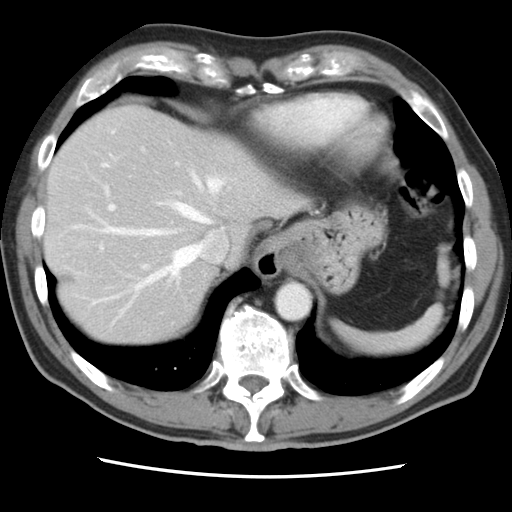
Contrast-enhanced abdominal CT, one axial slice. Position 69 of 83 along the scan axis. 120 kVp. Intravenous contrast given. Soft-tissue window (W 400 / L 40 HU). 5 mm slice thickness. 512 × 512 image matrix, field of view 321 × 321 mm. Male patient, age 69 years. Case-level facts recorded for this patient, not image findings: diagnosis: colorectal cancer liver metastases, imaged before liver resection; multiple liver metastases: yes; largest metastasis: 3.5 cm; disease in both lobes: no.
Outlined on this slice (expert manual segmentation):
- hepatic veins: bounding box (x1, y1, x2, y2) in pixels: (76, 131, 224, 311)
- liver: (45, 107, 295, 346)
- planned liver remnant (the part of the liver to remain after resection): (45, 148, 216, 346)
- portal vein (with intrahepatic branches): (99, 186, 181, 269)